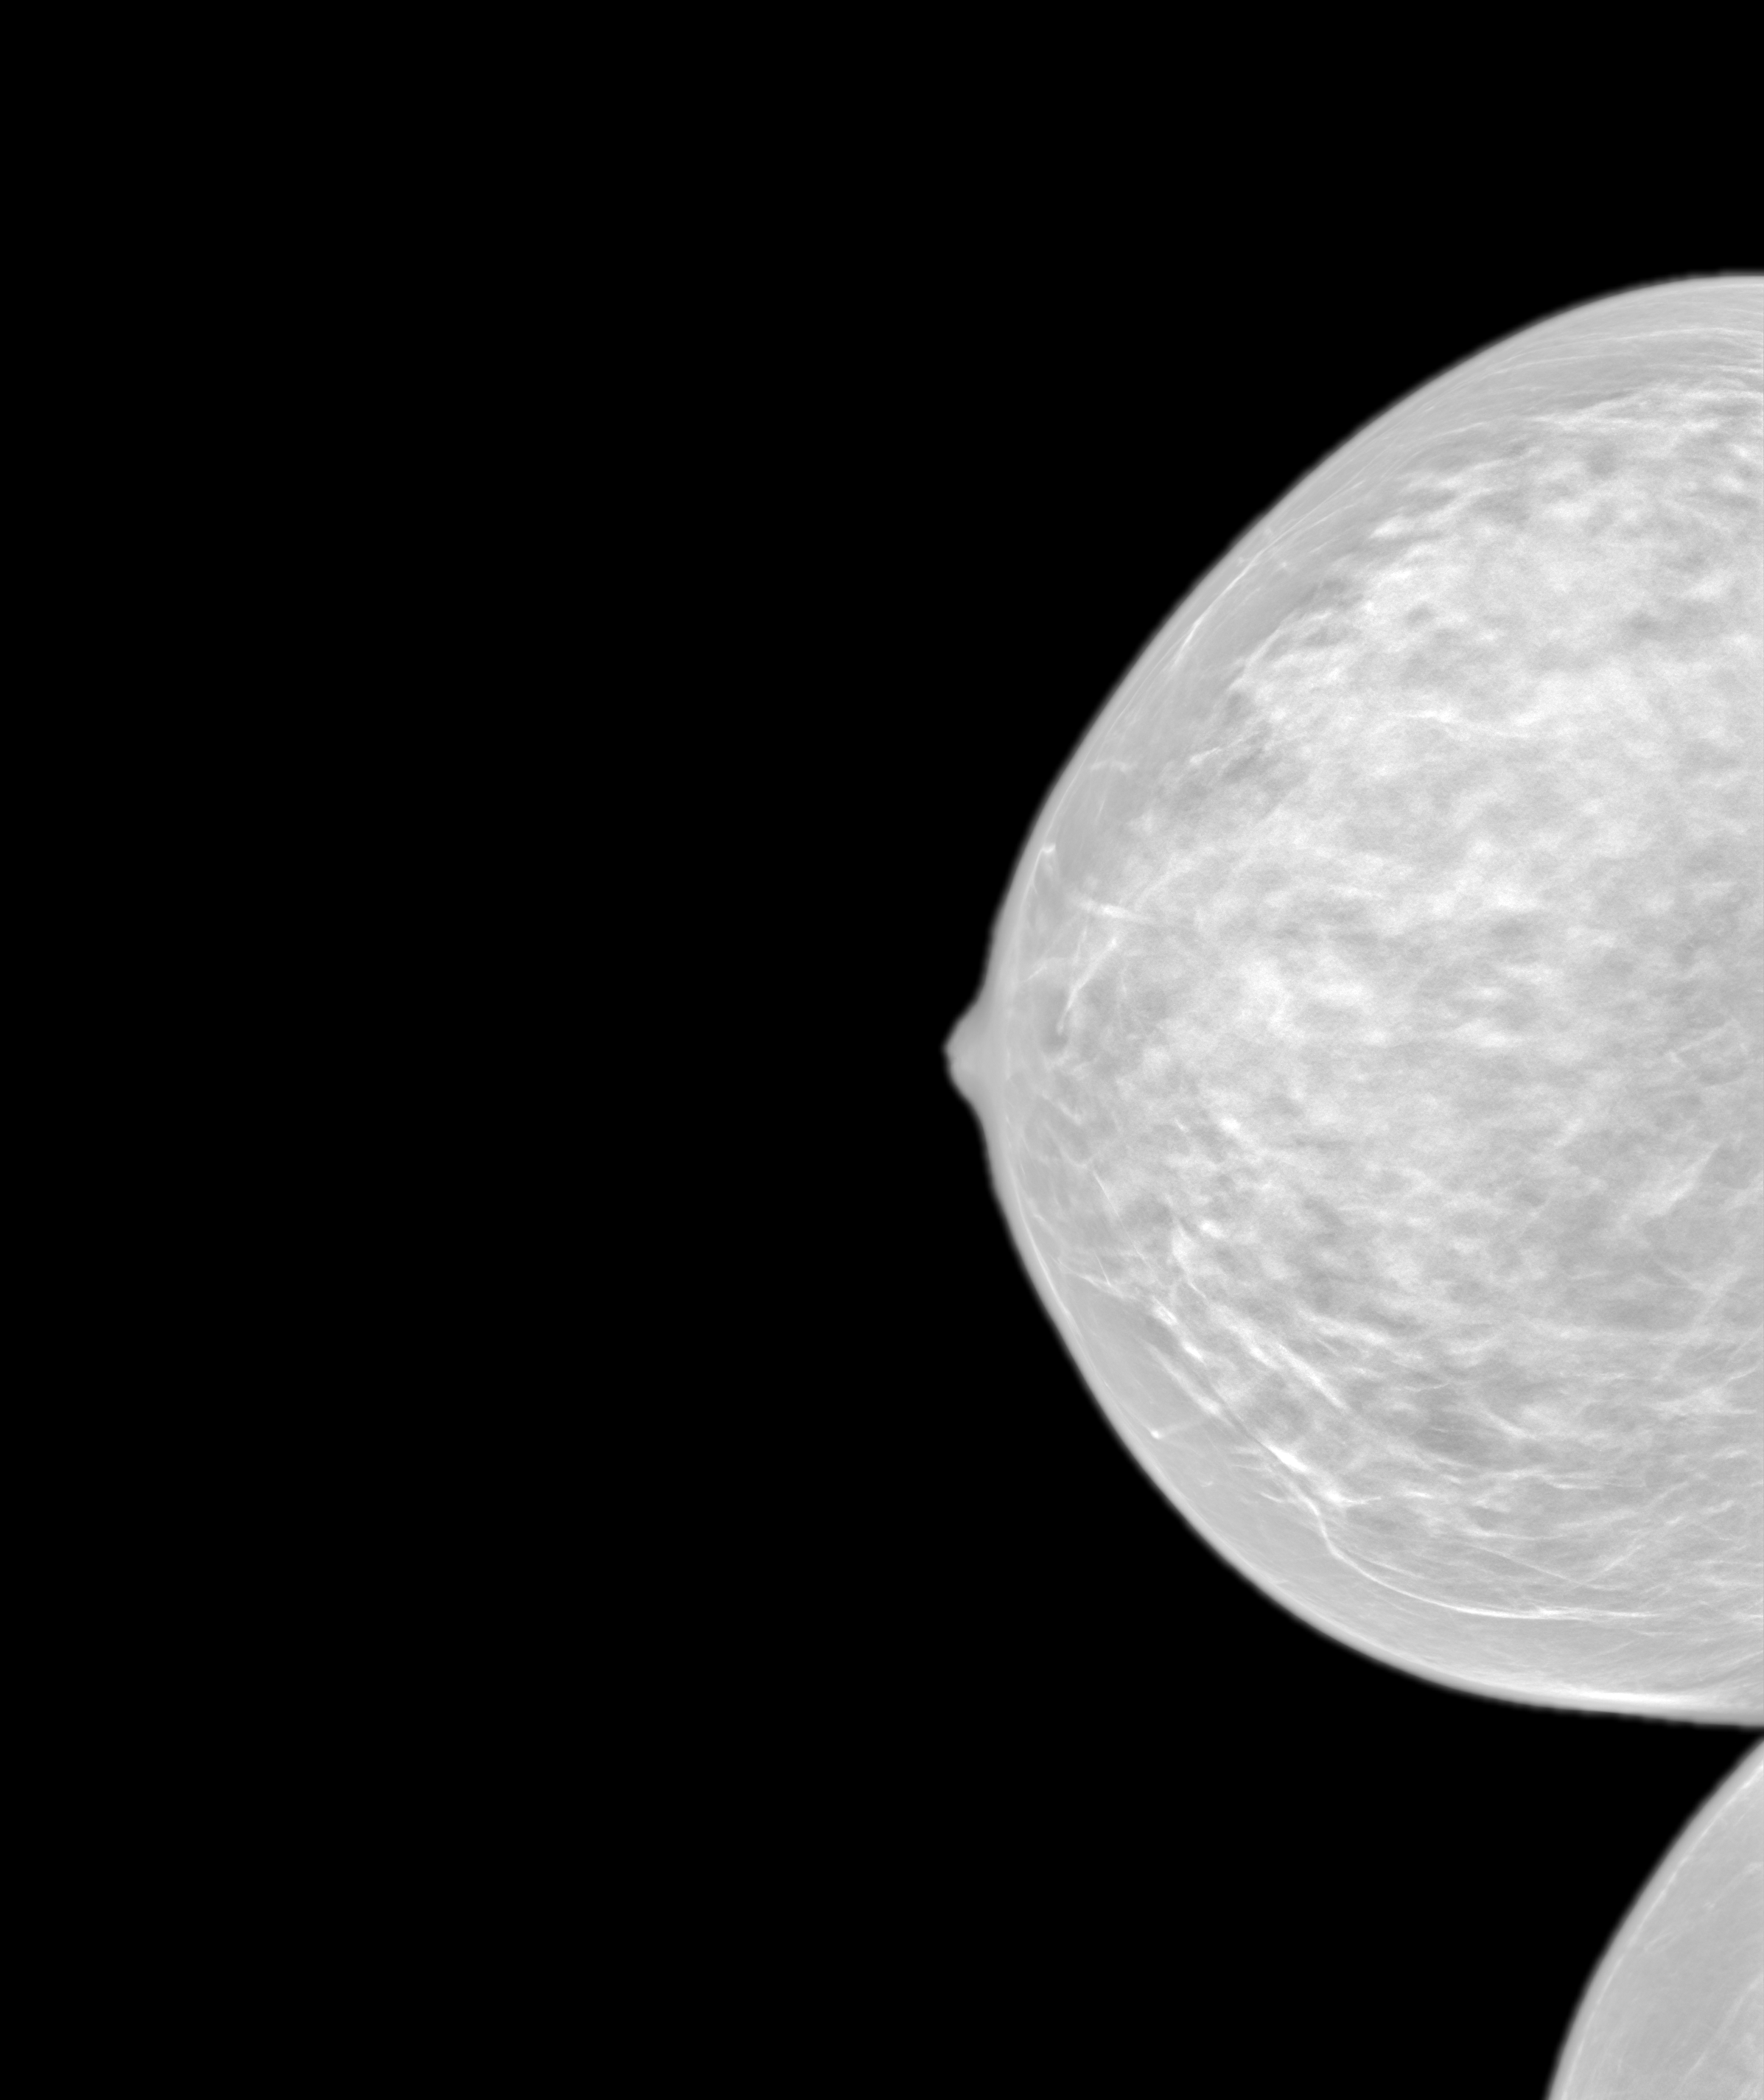
Screening examination. Female patient, age 42 years.
Image type: synthesized 2-D view from tomosynthesis. Breast: right. Projection: cranio-caudal projection.